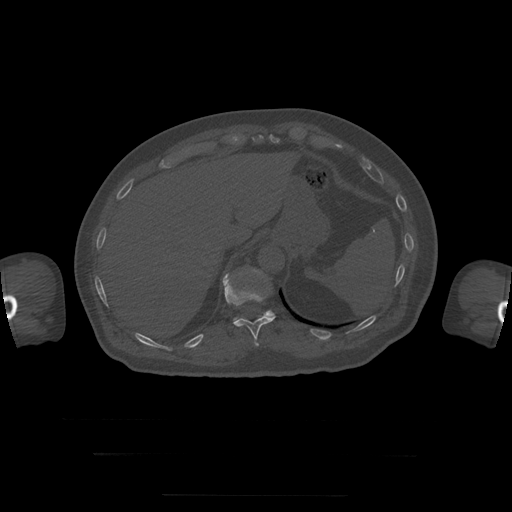
CT including the spine, one axial slice; position 93 of 397 along the scan axis; reconstruction kernel STANDARD; bone window (W 1800 / L 400 HU); 512 × 512 image matrix. Patient age 73 years. Case-level facts recorded for this patient, not image findings: primary cancer: prostate.
Annotated regions visible in this slice (semi-automatic segmentation, software-assisted and operator-edited):
- T11 vertebra: bounding box <223,274,276,346> (left, top, right, bottom; pixels)
- T12 vertebra: <234,270,275,321>